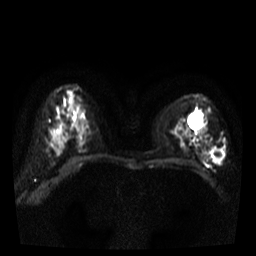
Breast MRI, one axial slice. Diffusion-weighted series; image 2 of 4 stored at this slice position (different b-values; order by instance number). 3 T. 5 mm slice thickness. 256 × 256 image matrix, field of view 320 × 320 mm. Female patient.
Structures marked on this image (outlined manually by an expert reader):
- tumour on diffusion-weighted imaging: bounding box (x1, y1, x2, y2) in pixels: (210, 147, 223, 163)